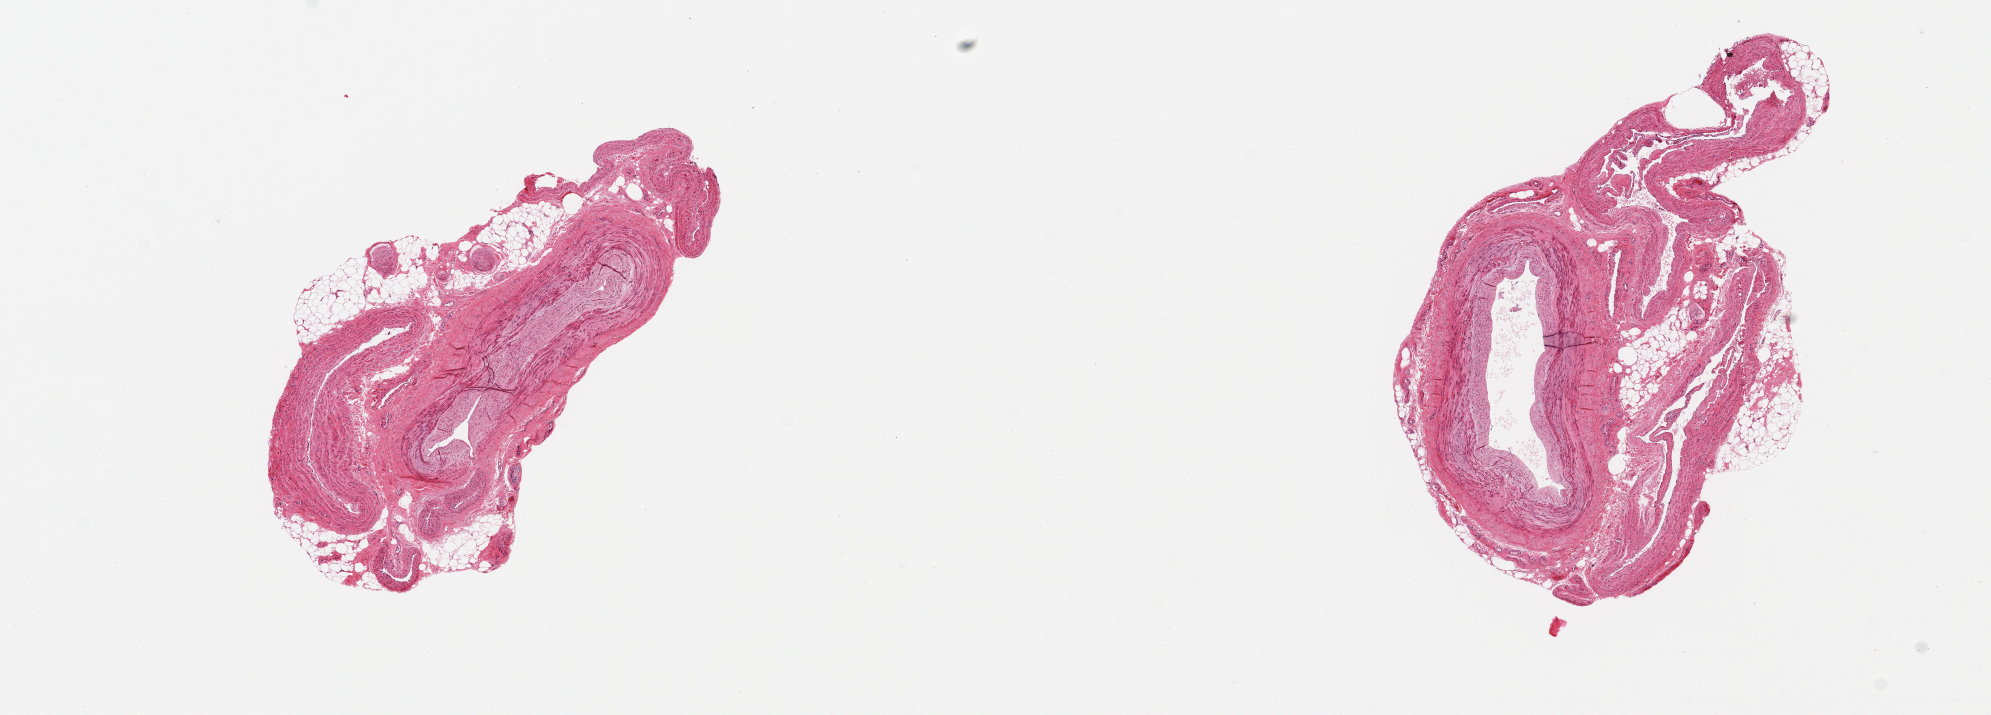
Digitized haematoxylin and eosin-stained section, brightfield, whole scanned area (about 15.8 x 5.7 mm, slide scanned at 20x) shown as a low-resolution overview. Donor: male.
Specimen: PAXgene-fixed, paraffin-embedded tissue; sampled site (target tissue): tibial artery; tissue donor sample.